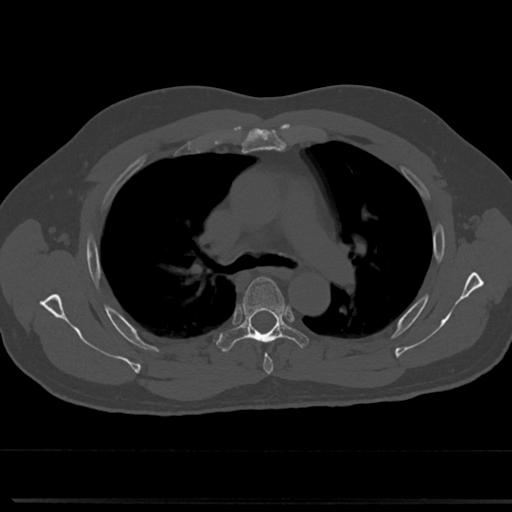
CT including the spine, one axial slice. Position 509 of 817 along the scan axis. 120 kVp. Bone window (W 1800 / L 400 HU). 512 × 512 image matrix, field of view 355 × 355 mm. Patient: male, 61 years. Case-level facts recorded for this patient, not image findings: primary cancer: prostate.
Outlined on this slice (semi-automatically segmented with operator editing):
- T4 vertebra: bounding box <241,335,284,373> (left, top, right, bottom; pixels)
- T5 vertebra: <218,275,310,352>